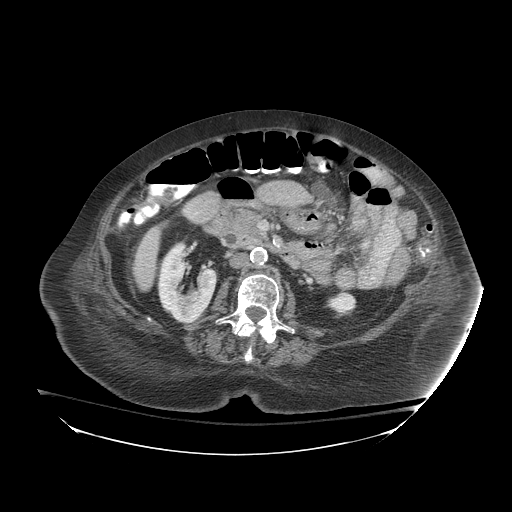
Contrast-enhanced abdominal CT (liver protocol), one axial slice; slice 23 of 81 in the series (ordered by position); reconstruction kernel STANDARD; soft-tissue window (W 400 / L 40 HU); 2.5 mm slice thickness; 512 × 512 image matrix, field of view 500 × 500 mm. From the clinical record (not read from this slice): diagnosis: hepatocellular carcinoma (patient treated with transarterial chemoembolisation; whether this scan precedes or follows treatment is not stated here); TNM stage (as recorded): Stage-I; Child-Pugh class: B; tumour differentiation: well-moderately differentiated; tumour nodularity: uninodular.
Annotated regions visible in this slice (semi-automatic segmentation, software-assisted and operator-edited):
- liver parenchyma outside the tumour (the mass and vessels are separate outlines, so this box may not span the whole liver): box from (x=132, y=226) to (x=160, y=290) px